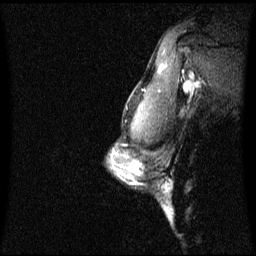
Breast MRI (dynamic contrast-enhanced), one sagittal slice. Position 53 of 60 along the scan axis. Dynamic contrast-enhanced series, image 2 of 3 at this slice position (ordered by acquisition). 1.5 T. TE 4.2 ms, TR 8.4 ms. 256 × 256 image matrix, field of view 240 × 240 mm. Patient: female, 42 years. Case-level facts recorded for this patient, not image findings: setting: breast cancer imaged before/during neoadjuvant chemotherapy; receptor status: triple-negative.
Annotated regions visible in this slice (semi-automatic segmentation, software-assisted and operator-edited):
- analysis volume of interest (the breast-tissue region the enhancement analysis was run in; not a lesion): box from (x=107, y=156) to (x=138, y=185) px
- tumour enhancement mask (voxels above the 70 % enhancement threshold inside the analysis volume of interest): (x=133, y=168)–(x=136, y=173)